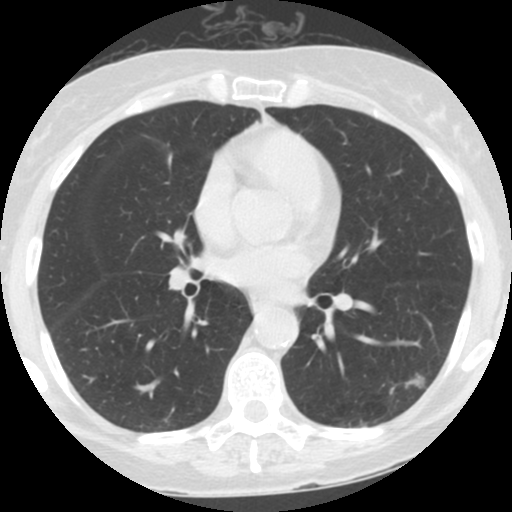
Low-dose screening chest CT, one axial slice. Position 69 of 152 along the scan axis. Lung window (W 1500 / L -600 HU). 512 × 512 image matrix, field of view 280 × 280 mm.
Annotated regions visible in this slice (manually delineated by an expert):
- lesion 1 (tumor, lower lobe of left lung): bounding box (x1, y1, x2, y2) in pixels: (405, 374, 424, 389)